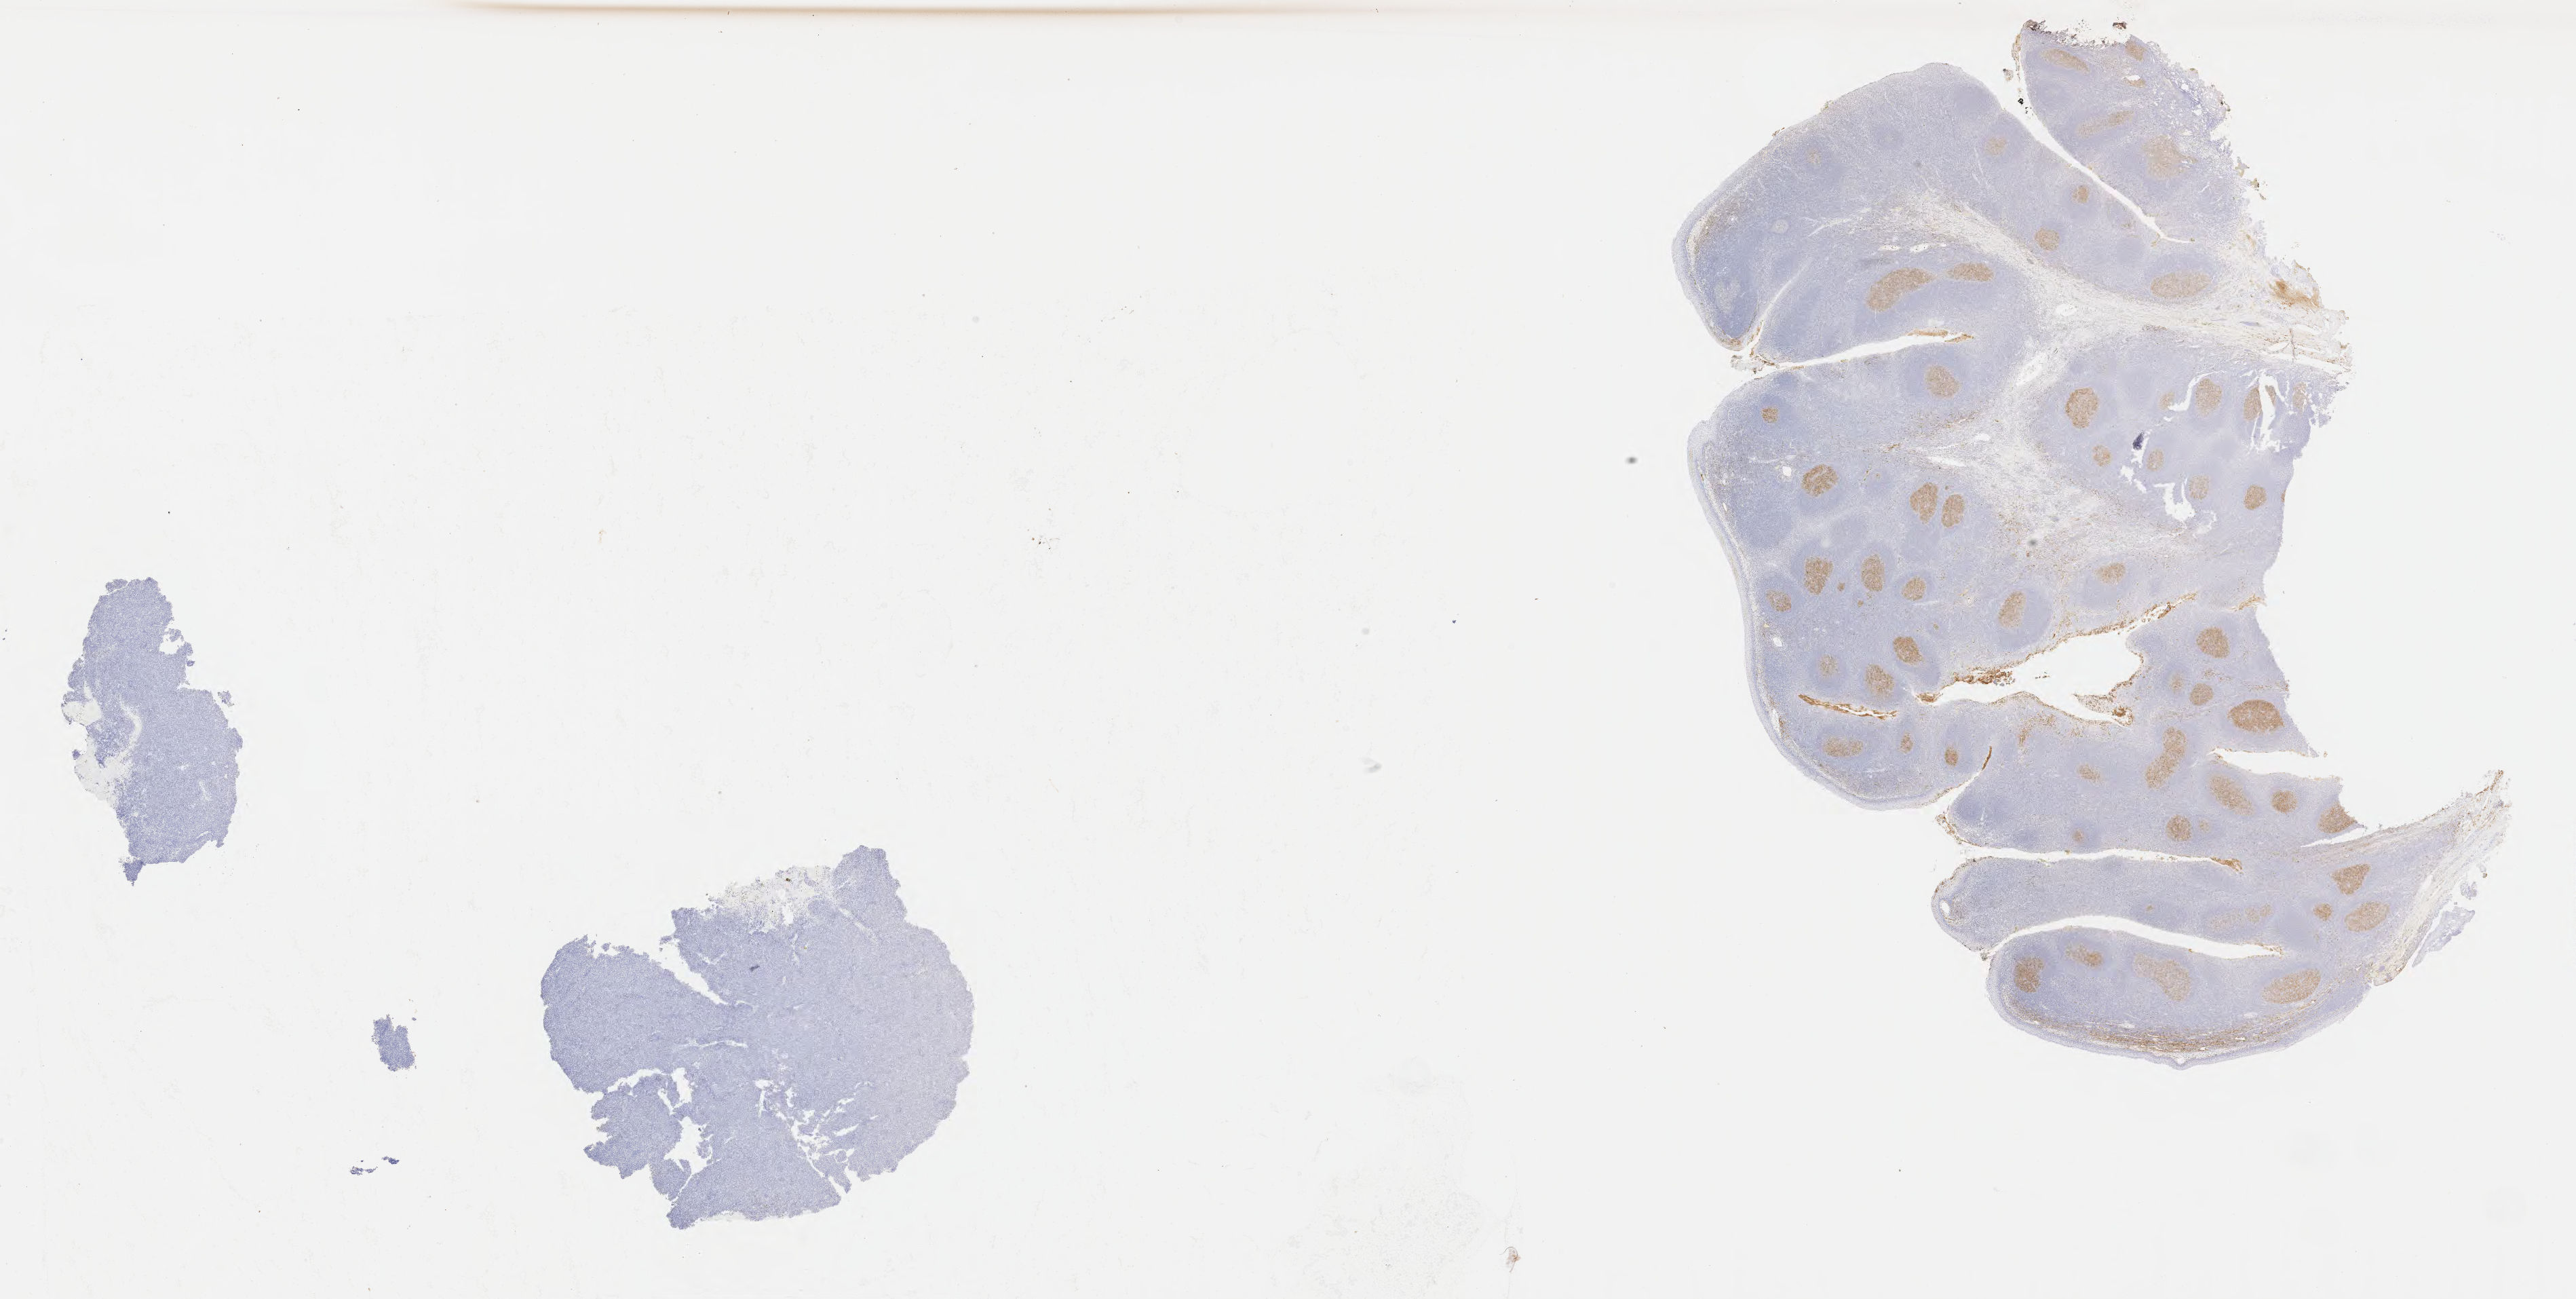
Whole-slide image, immunohistochemical stain for CD10 — whole scanned area (about 30.7 x 15.5 mm) shown as a low-resolution overview, specimen: tumor tissue, anatomic site: lymph node. Female patient, age 51 years.
Histologic diagnosis: Diffuse large B-cell lymphoma, NOS.